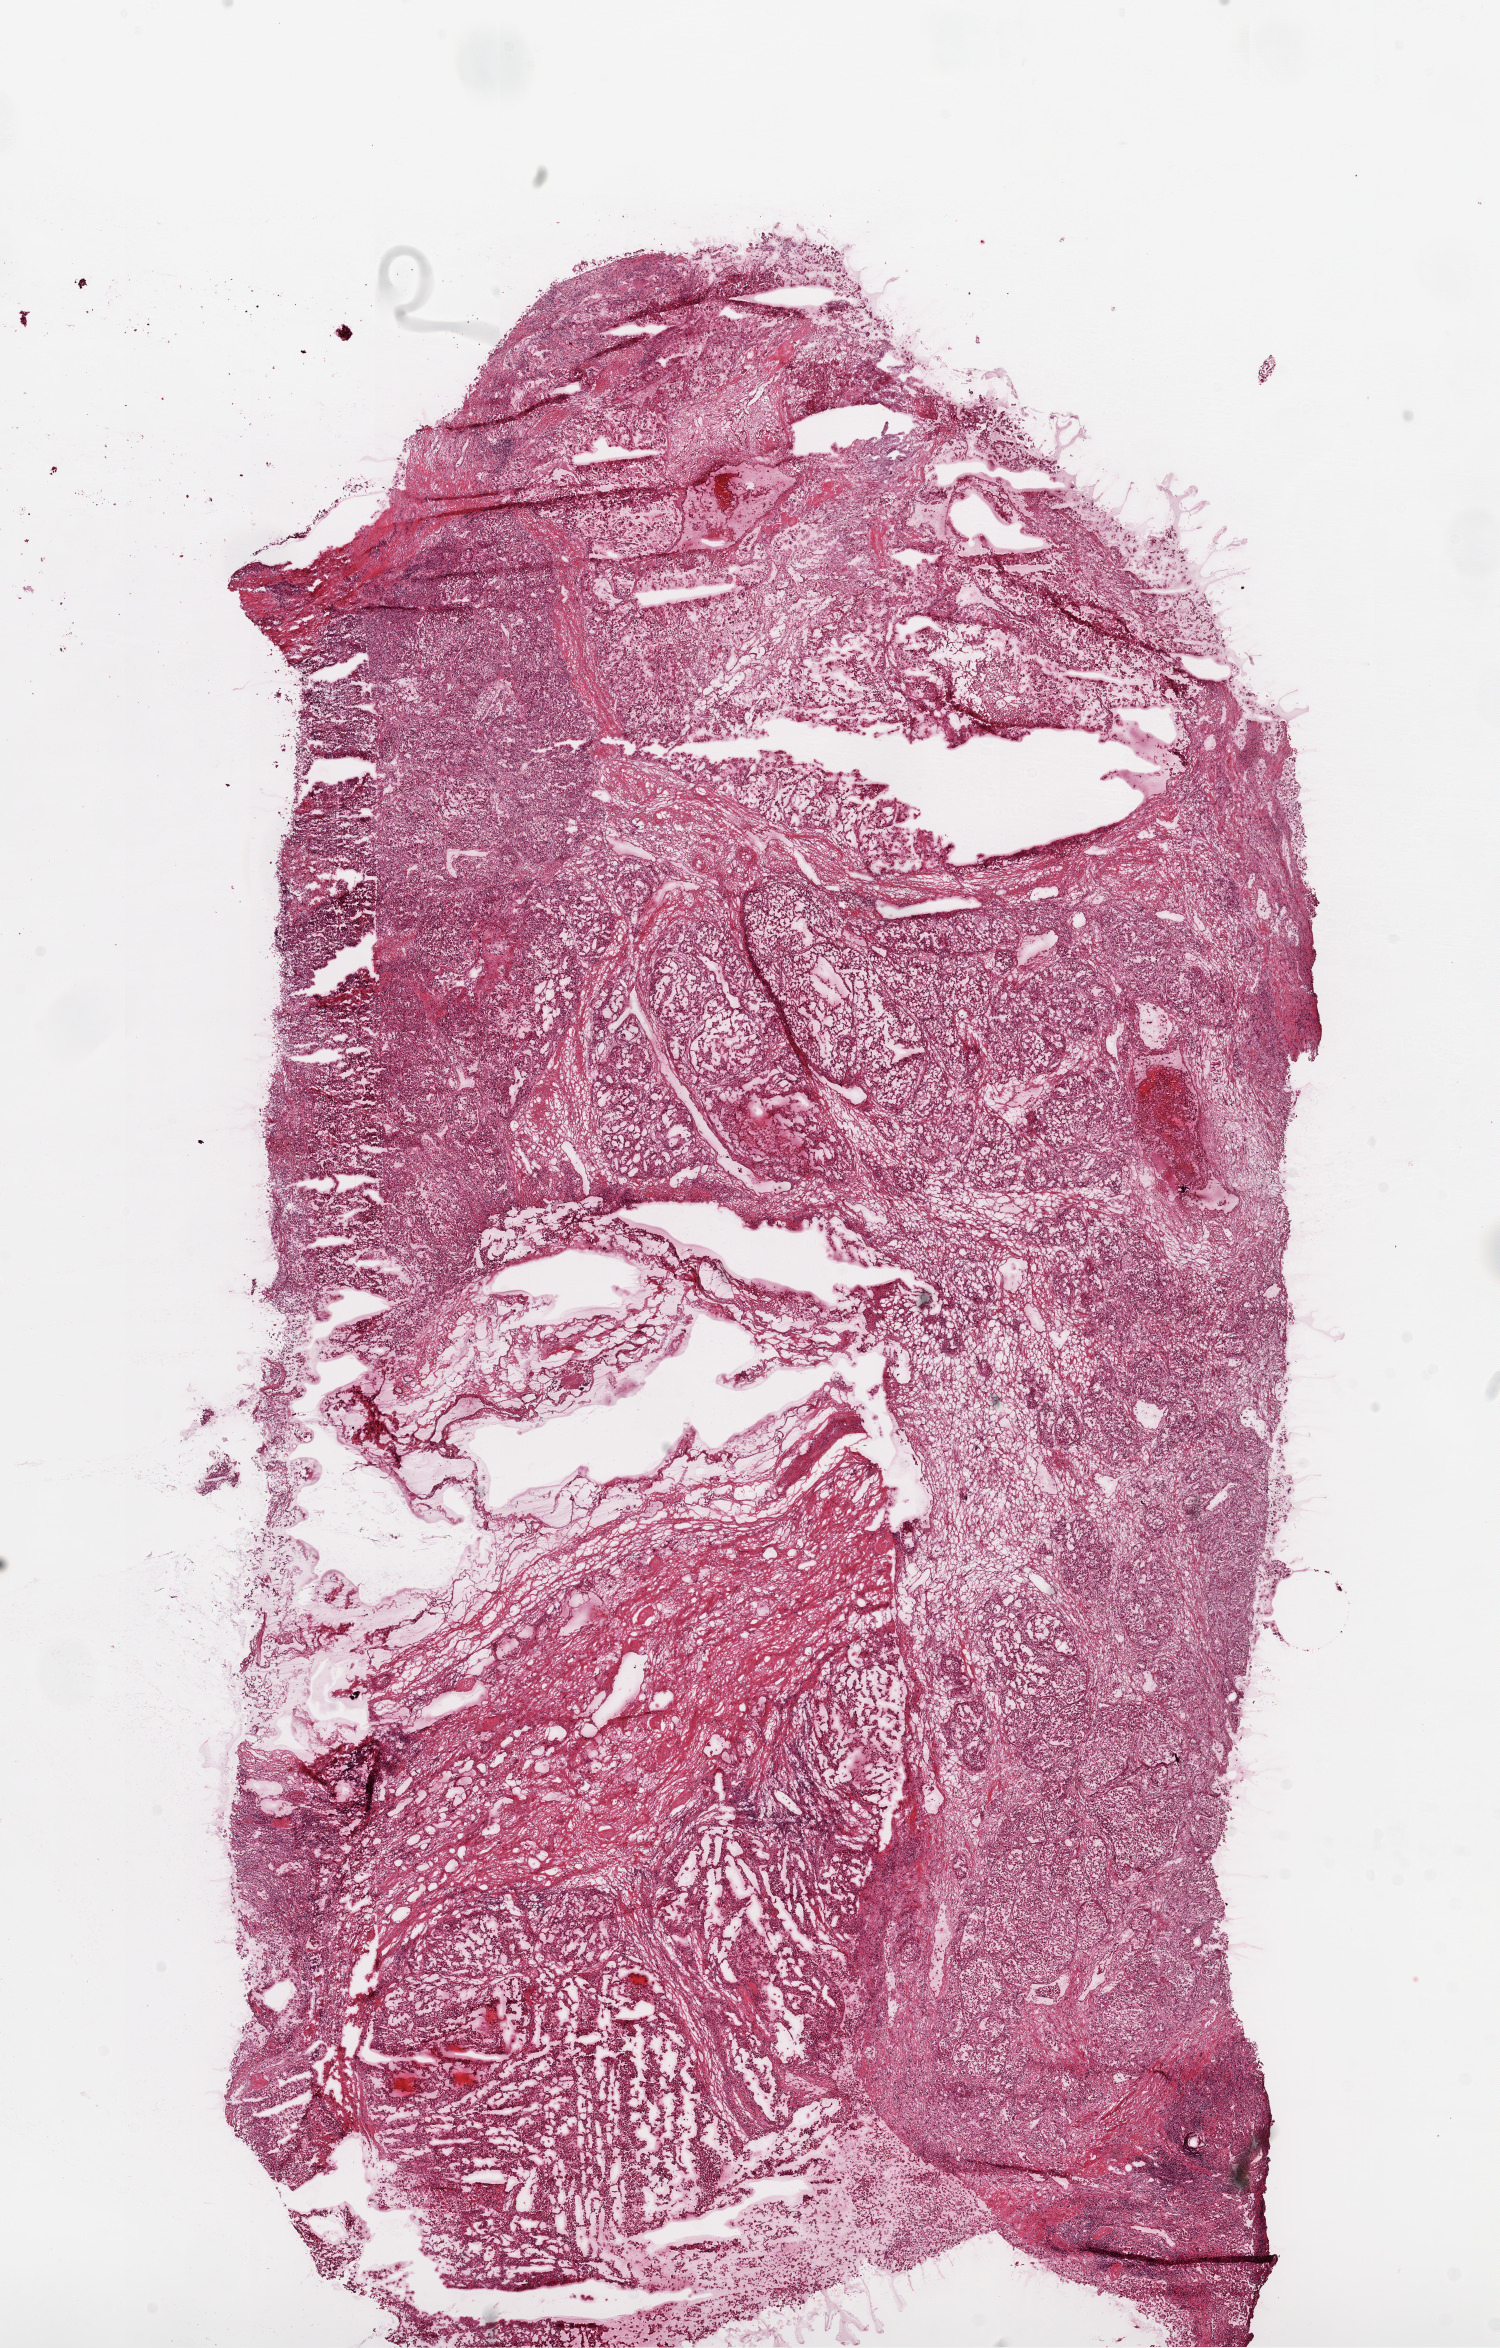
H&E whole-slide image, shown as a low-resolution overview of the whole scanned area (about 12.0 x 18.8 mm); frozen section from the top of the tissue portion; sample: primary tumour, kidney. Female patient; age at initial diagnosis 76 years. Histologic grade: G4 (undifferentiated). Composition of this section per pathologist review: tumour cells 75%, tumour nuclei 70%, normal cells 0%, stromal cells 25%, necrosis 0%.
AJCC pathologic stage: III. Lymph nodes positive (case pathology): 0 of 4 examined. Pathologic diagnosis: Clear cell adenocarcinoma, NOS.